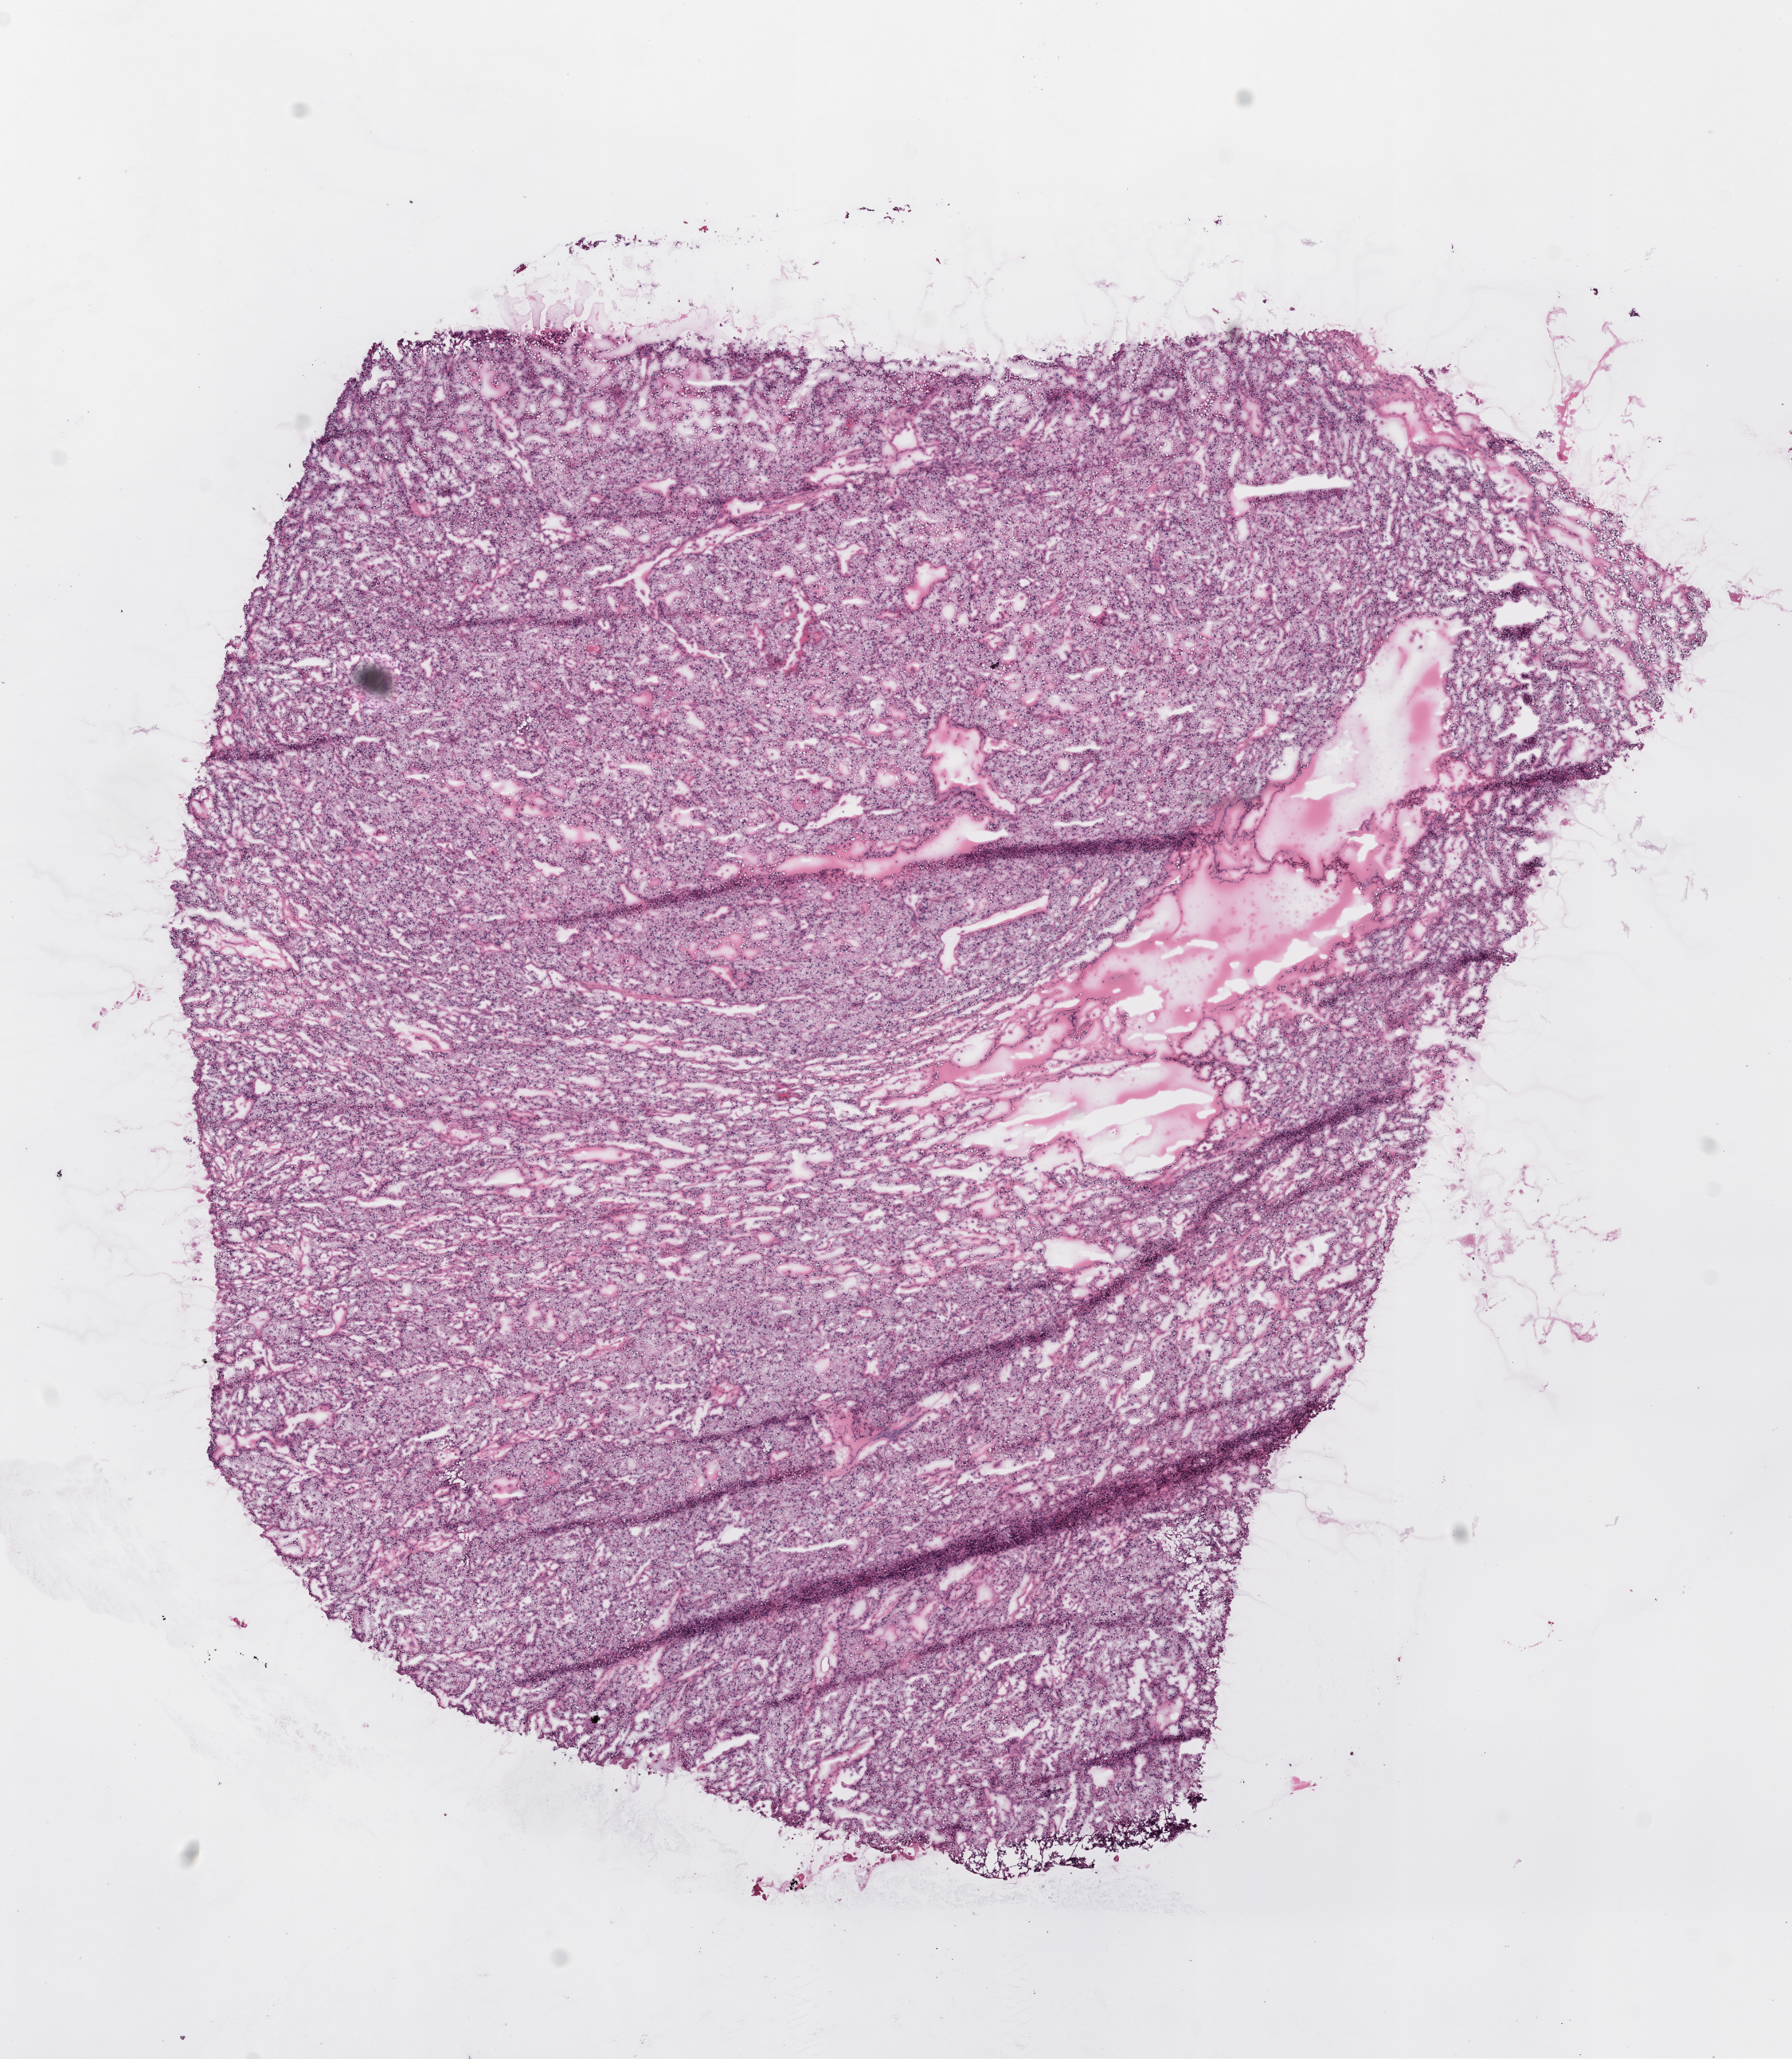
Hematoxylin and eosin (H&E) stained whole-slide image — low-resolution overview of the scanned area, about 9.0 x 10.4 mm (acquisition: 20x scan). Frozen section from the top of the tissue portion. Primary tumour sample from the kidney. Patient: male, age at initial diagnosis 40 years. Histologic grade: G2 (moderately differentiated). Composition of this section per pathologist review: tumour cells 90%, tumour nuclei 85%, normal cells 0%, stromal cells 10%, necrosis 0%.
AJCC pathologic stage: IV. Laterality: left. Diagnosis: Clear cell adenocarcinoma, NOS.